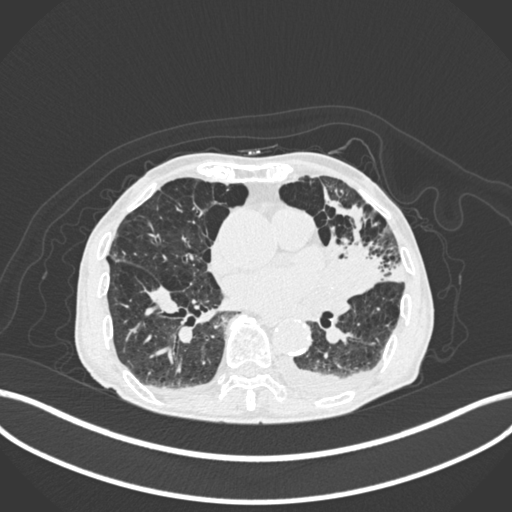
Chest CT, one axial slice; position 94 of 400 along the scan axis; 120 kVp; lung window (W 1500 / L -600 HU); 1 mm slice thickness; 512 × 512 image matrix, field of view 400 × 400 mm. Male patient, age 90 years or older. From the clinical record (not read from this slice): clinical TNM (as recorded): T2b N1 M0.
Structures marked on this image (rectangle marked by the reading radiologist):
- lung tumour (recorded histology: squamous cell carcinoma): bounding box (x1, y1, x2, y2) in pixels: (325, 226, 387, 301)